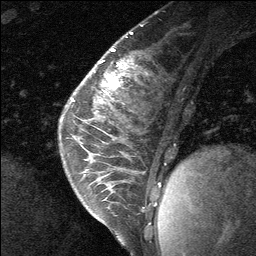
Breast MRI (dynamic contrast-enhanced), one sagittal slice. Slice 25 of 64 in the series (ordered by position). Dynamic contrast-enhanced study with each time point stored as its own series, time point 2 of 3 at this slice position (early post-contrast, ordered by acquisition time). 1.5 T. TE 4.8 ms, TR 27 ms. 256 × 256 image matrix. Patient: female, 26 years. From the clinical record (not read from this slice): setting: breast cancer imaged before/during neoadjuvant chemotherapy; receptor status: HR-positive, HER2-negative.
Outlined on this slice (semi-automatic segmentation, software-assisted and operator-edited):
- analysis volume of interest (the breast-tissue region the enhancement analysis was run in; not a lesion): bounding box <86,43,130,138> (left, top, right, bottom; pixels)
- tumour enhancement mask (voxels above the 90 % enhancement threshold inside the analysis volume of interest): <108,76,116,85>